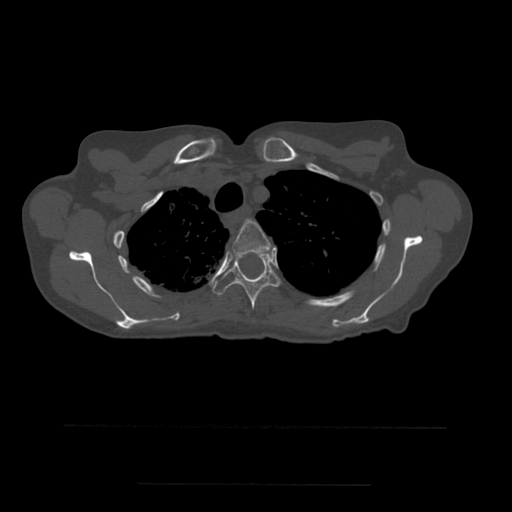
CT including the spine, one axial slice. Bone window (W 1800 / L 400 HU). 1.25 mm slice thickness. 512 × 512 image matrix. Patient age 58 years. From the clinical record (not read from this slice): primary cancer: lung.
Outlined on this slice (semi-automatic segmentation, software-assisted and operator-edited):
- T3 vertebra: box from (x=233, y=220) to (x=271, y=255) px
- T4 vertebra: (x=213, y=252)–(x=281, y=310)